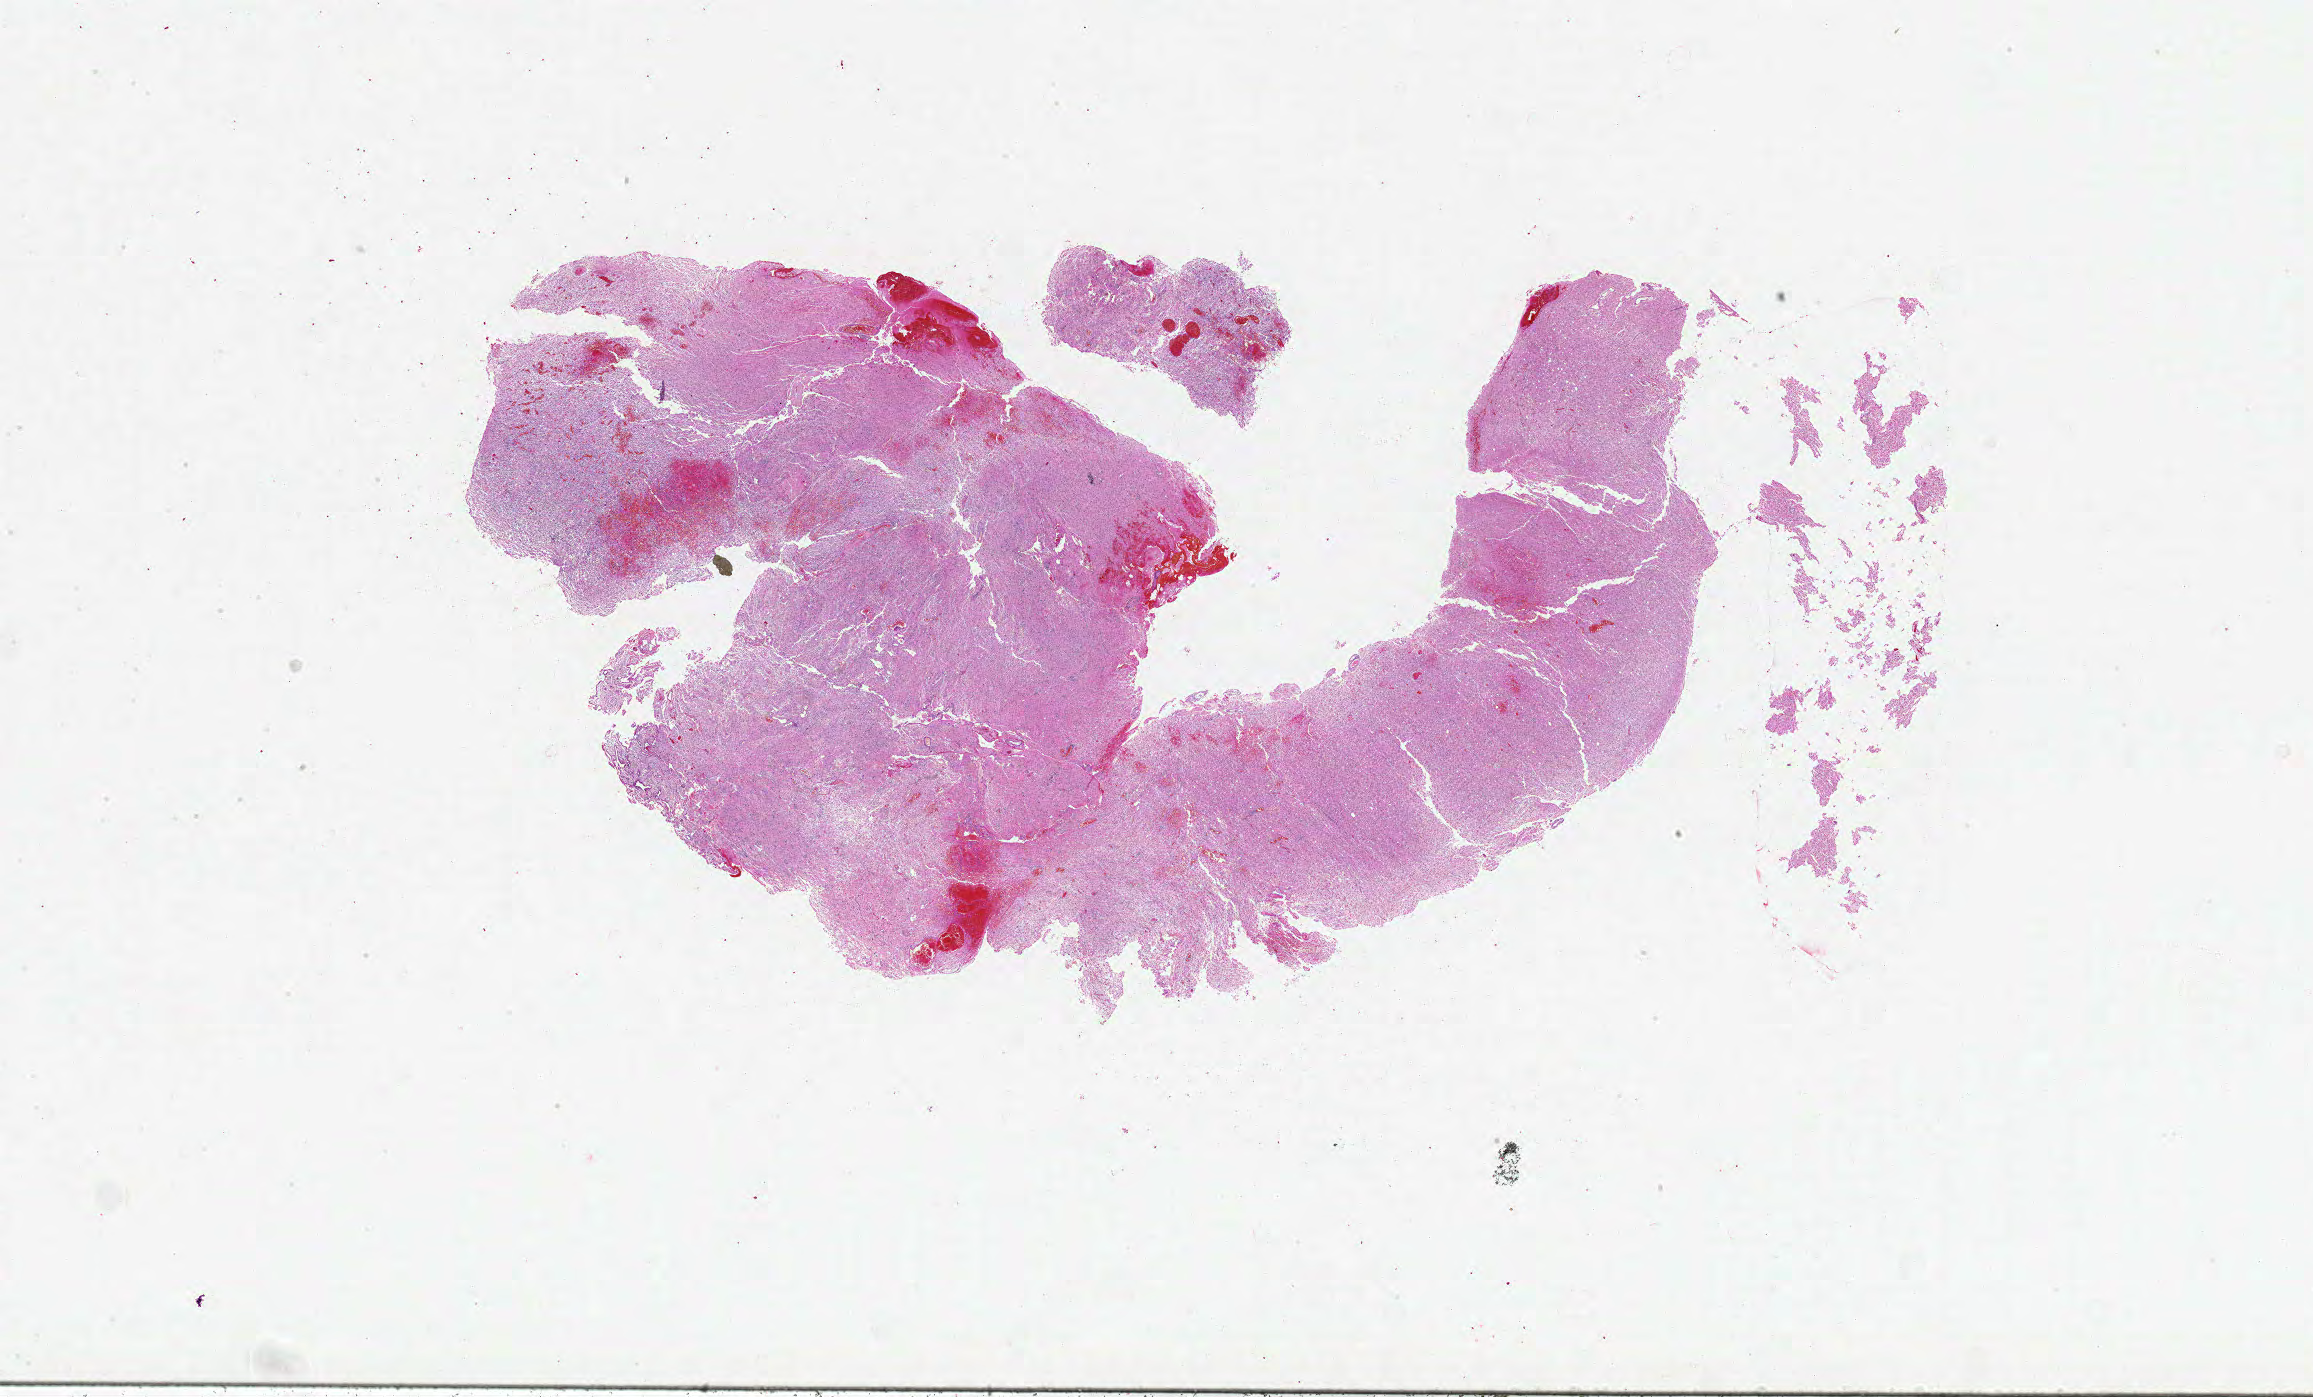
H&E-stained whole-slide image — a low-resolution overview of the entire scanned area, about 37.0 x 22.3 mm (slide scanned at 20x). Formalin-fixed paraffin-embedded (FFPE) diagnostic section. Brain, primary tumour sample. Patient: male, age at initial diagnosis 61 years.
Pathologic diagnosis: Glioblastoma.